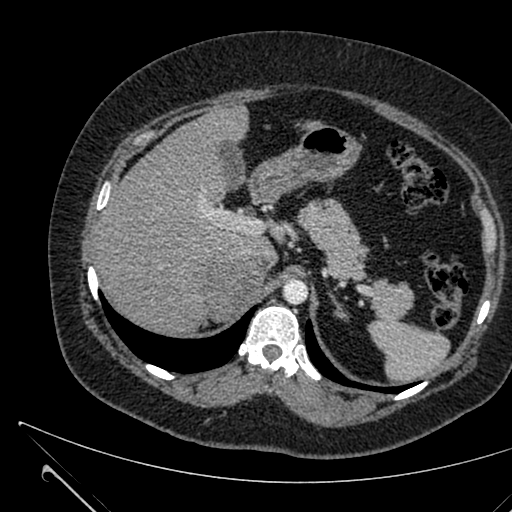
Contrast-enhanced abdominal CT, one axial slice; position 468 of 731 along the scan axis; 120 kVp; intravenous contrast given; soft-tissue window (W 400 / L 40 HU); 512 × 512 image matrix, field of view 376 × 376 mm. Female patient, age 36 years. From the clinical record (not read from this slice): diagnosis: adrenocortical carcinoma; tumour side: right adrenal; tumour size at pathology: 10 cm.
Structures marked on this image (semi-automatically segmented with operator editing):
- mass: bounding box (x1, y1, x2, y2) in pixels: (206, 257, 268, 319)